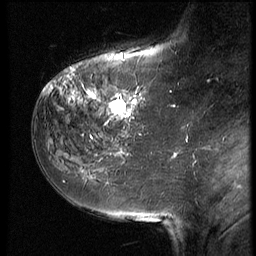
Breast MRI (dynamic contrast-enhanced), one sagittal slice; slice 19 of 64 in the series (ordered by position); 3 images stored at this slice position (order not interpretable as contrast timing); 1.5 T; TE 4.2 ms, TR 9 ms; 2.5 mm slice thickness; 256 × 256 image matrix, field of view 180 × 180 mm. Patient: female, 59 years. From the clinical record (not read from this slice): setting: breast cancer imaged before/during neoadjuvant chemotherapy; receptor status: HER2-positive.
Structures marked on this image (semi-automatic segmentation, software-assisted and operator-edited):
- analysis volume of interest (the breast-tissue region the enhancement analysis was run in; not a lesion): bounding box (x1, y1, x2, y2) in pixels: (54, 65, 155, 132)
- tumour enhancement mask (voxels above the 140 % enhancement threshold inside the analysis volume of interest): (55, 68, 145, 120)